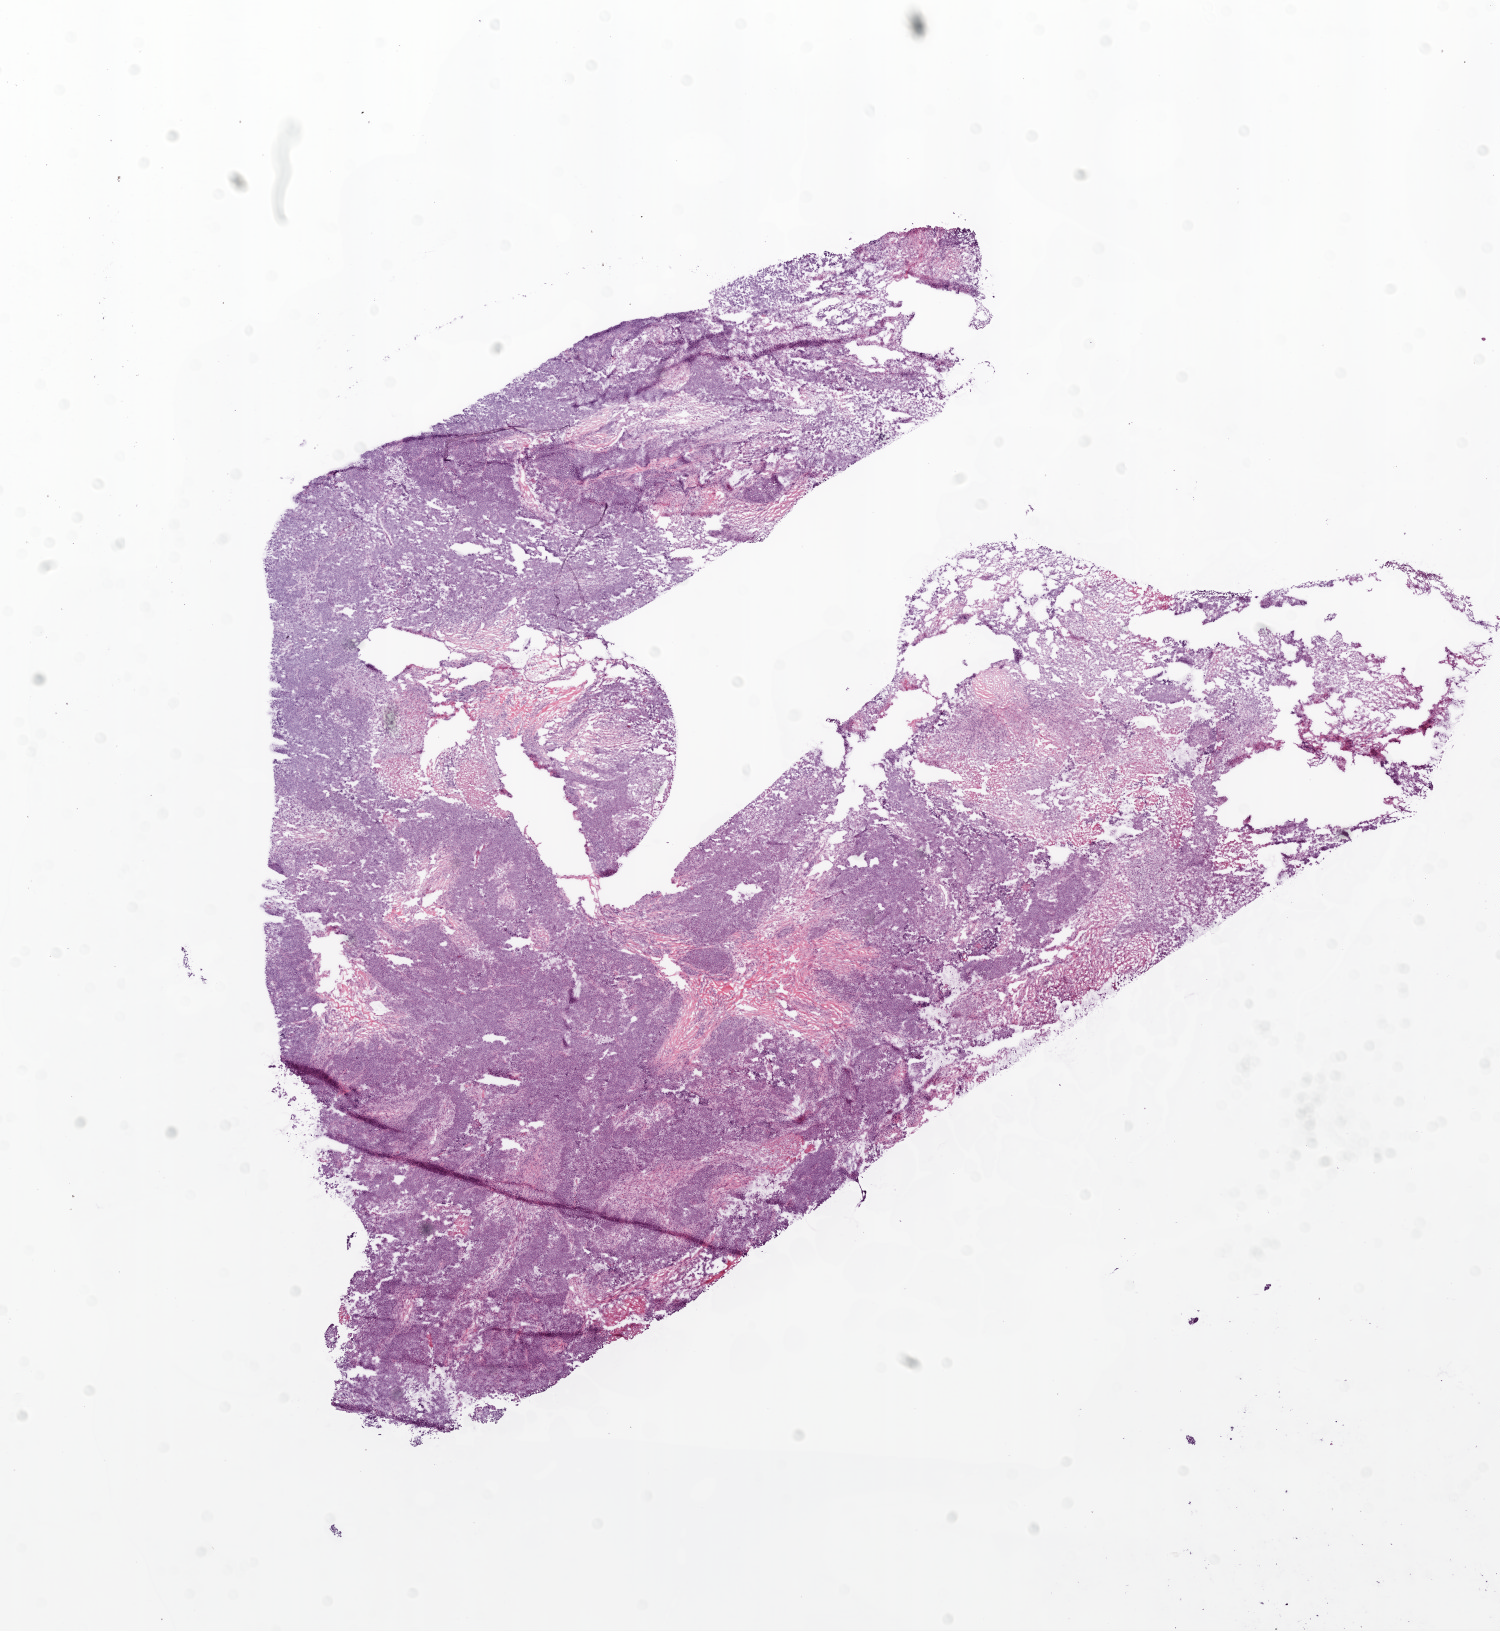
Whole-slide histology image, H&E-stained — low-resolution overview of the scanned area, about 12.0 x 13.1 mm (slide scanned at 20x). Frozen section. Sample: primary tumour, ovary. Female, age 60 years at initial diagnosis. Histologic grade: G3 (poorly differentiated). Composition of this section per pathologist review: tumour cells 80%, tumour nuclei 90%, normal cells 0%, stromal cells 18%, necrosis 2%.
• diagnosis: Serous cystadenocarcinoma, NOS
• FIGO stage: IIIB